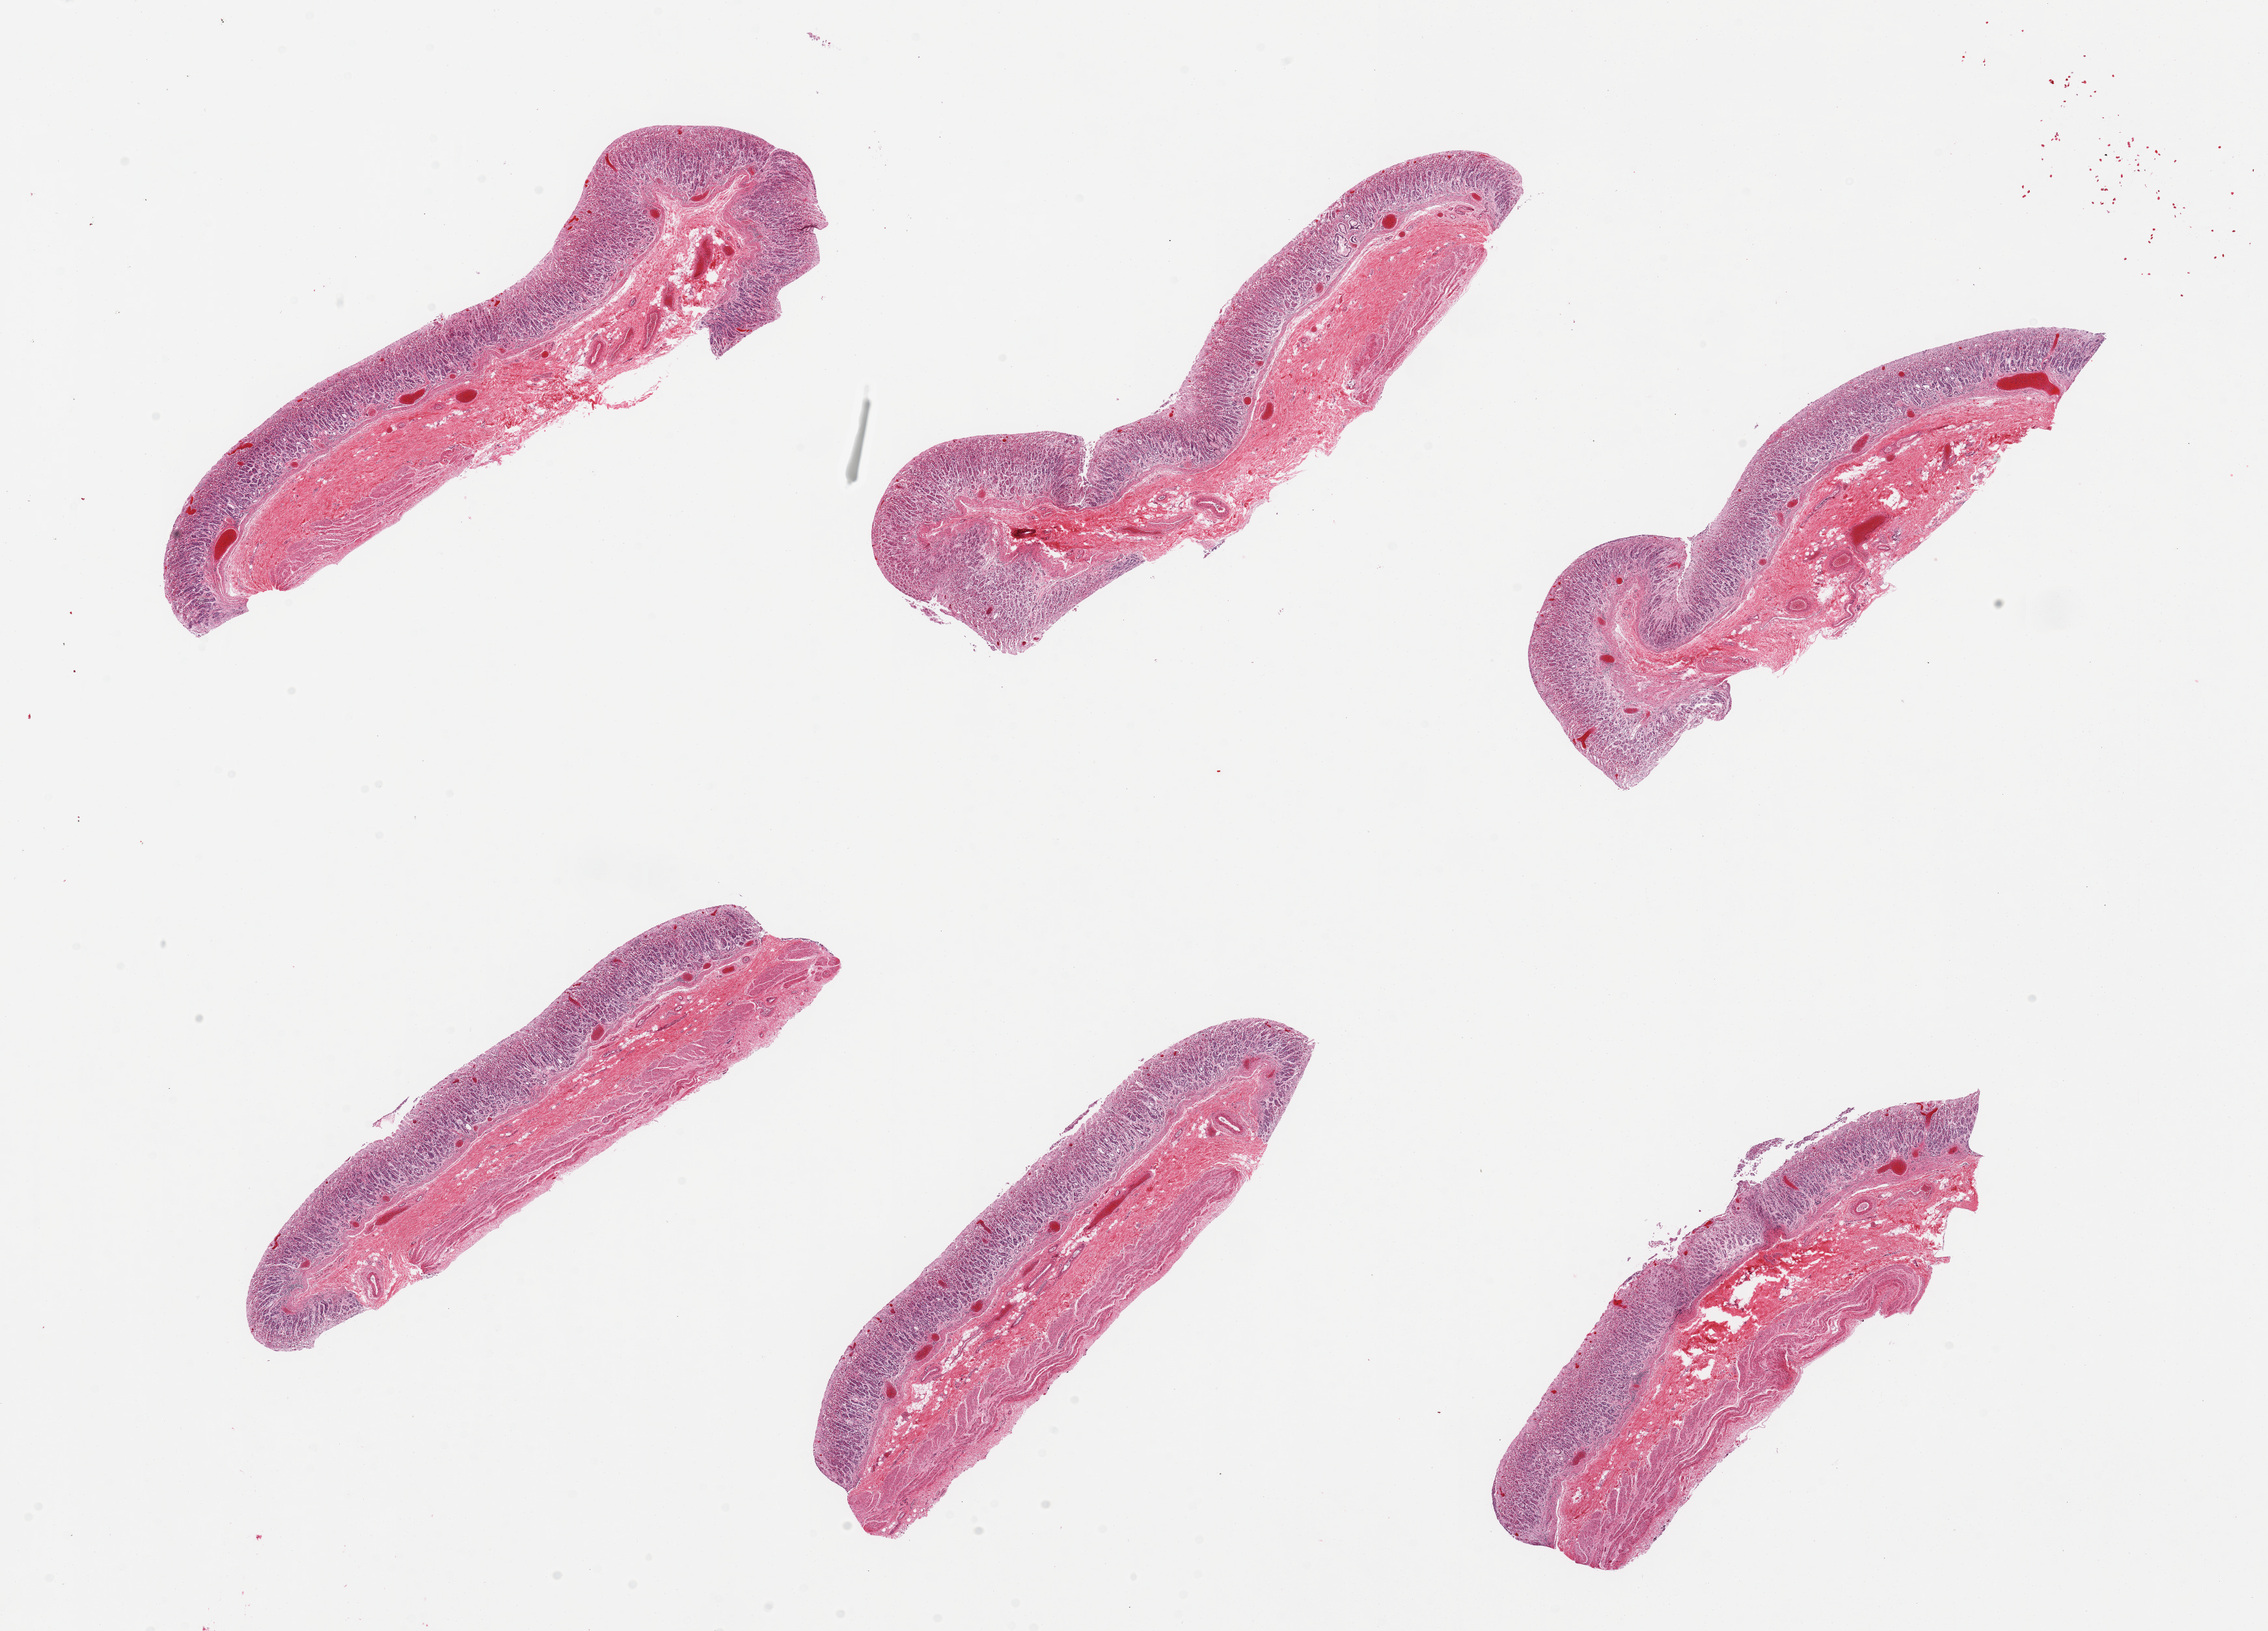
Digitized hematoxylin and eosin (H&E)-stained section — low-resolution overview of the scanned area, about 27.6 x 19.8 mm (acquisition: 20x scan). PAXgene-fixed, paraffin-embedded tissue. Sampled site (target tissue): stomach. Donor tissue sample. Donor: male.
• reviewer comment on this tissue sample: 6 pieces mucosa ~0.7mm, up ~30% total thickness, but severly autolyzed